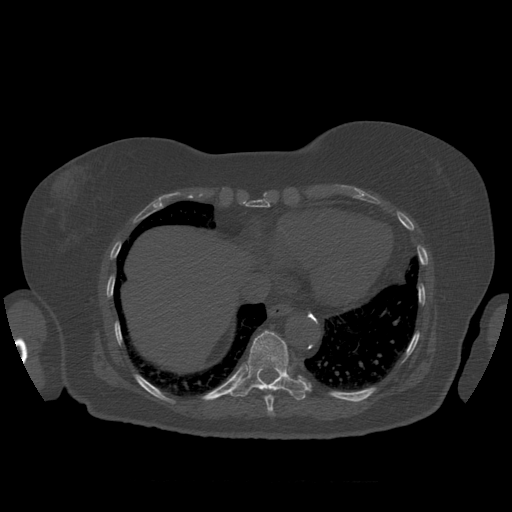
CT including the spine, one axial slice; slice 345 of 399 in the series (ordered by position); bone window (W 1800 / L 400 HU); 512 × 512 image matrix, field of view 404 × 404 mm. Patient age 81 years. From the clinical record (not read from this slice): primary cancer: renal.
Structures marked on this image (semi-automatic segmentation, software-assisted and operator-edited):
- T10 vertebra: bounding box [x1, y1, x2, y2] px = [230, 331, 310, 400]
- T9 vertebra: [265, 395, 275, 416]